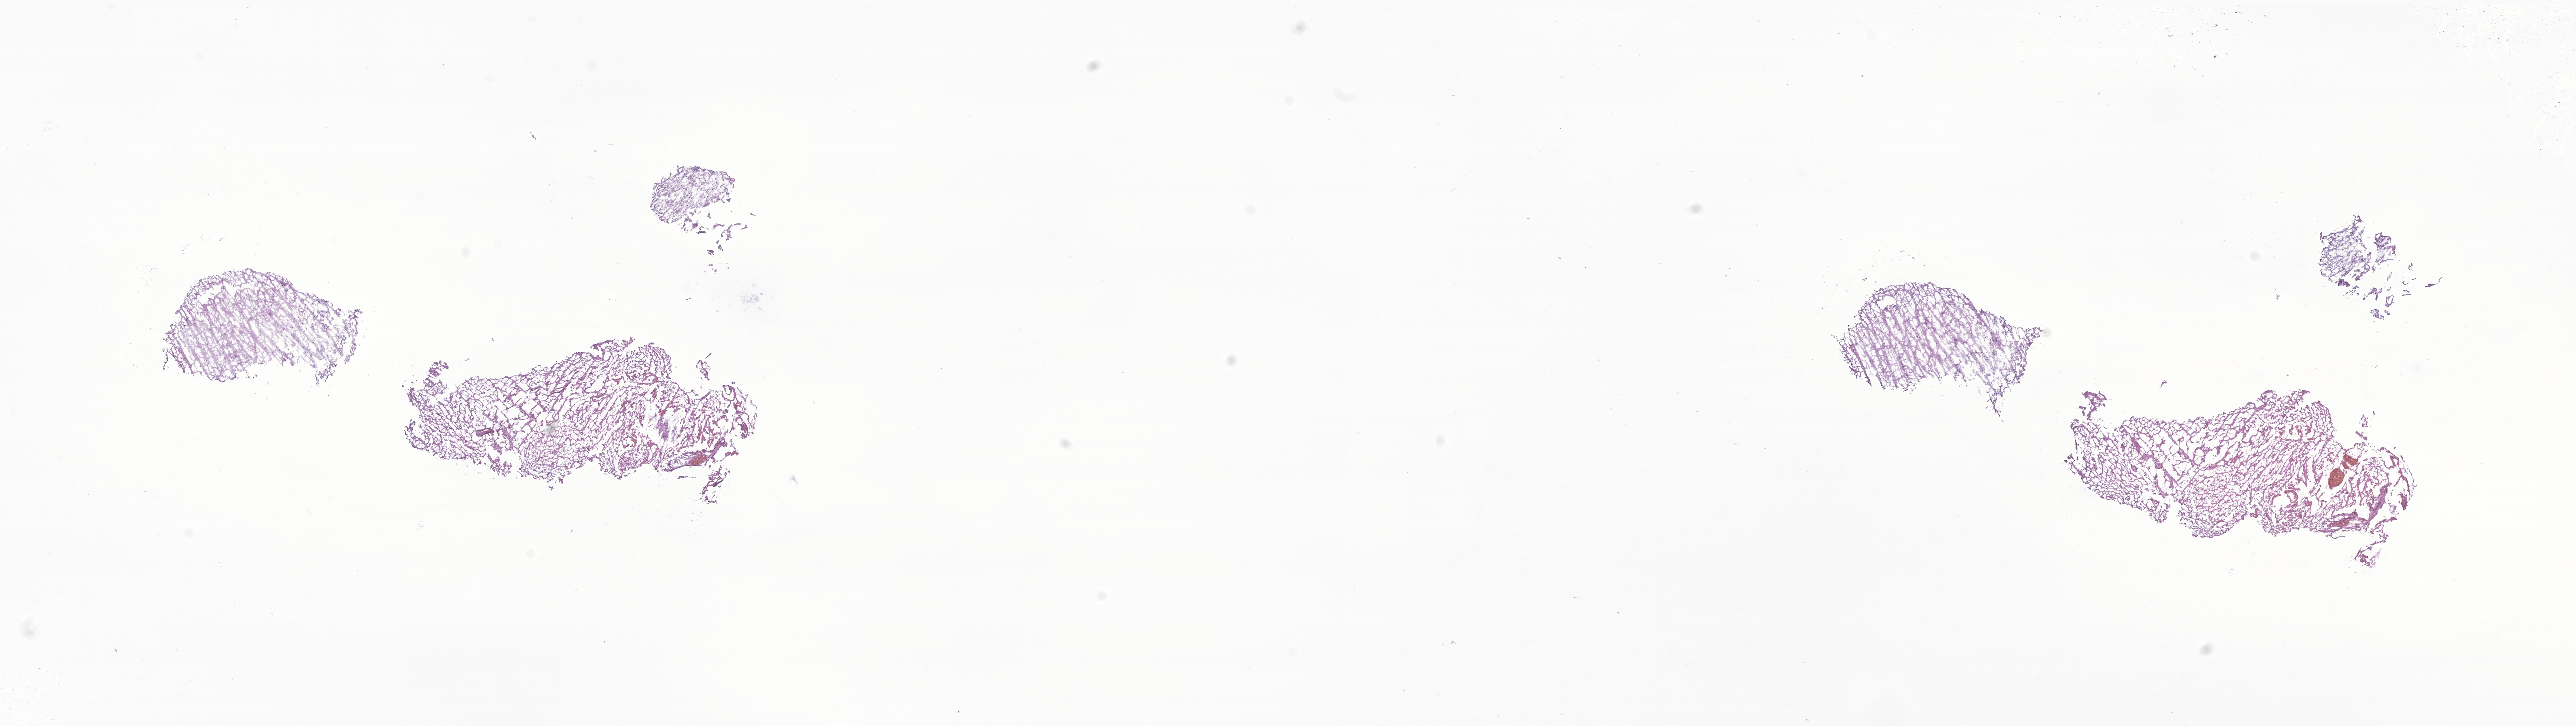
Digitized haematoxylin and eosin-stained section of tumor tissue from the temporal lobe — low-resolution overview of the scanned area, about 29.3 x 8.2 mm. Frozen section (OCT-embedded). Patient: male, age 188 months.
• recorded diagnosis: Pilocytic astrocytoma